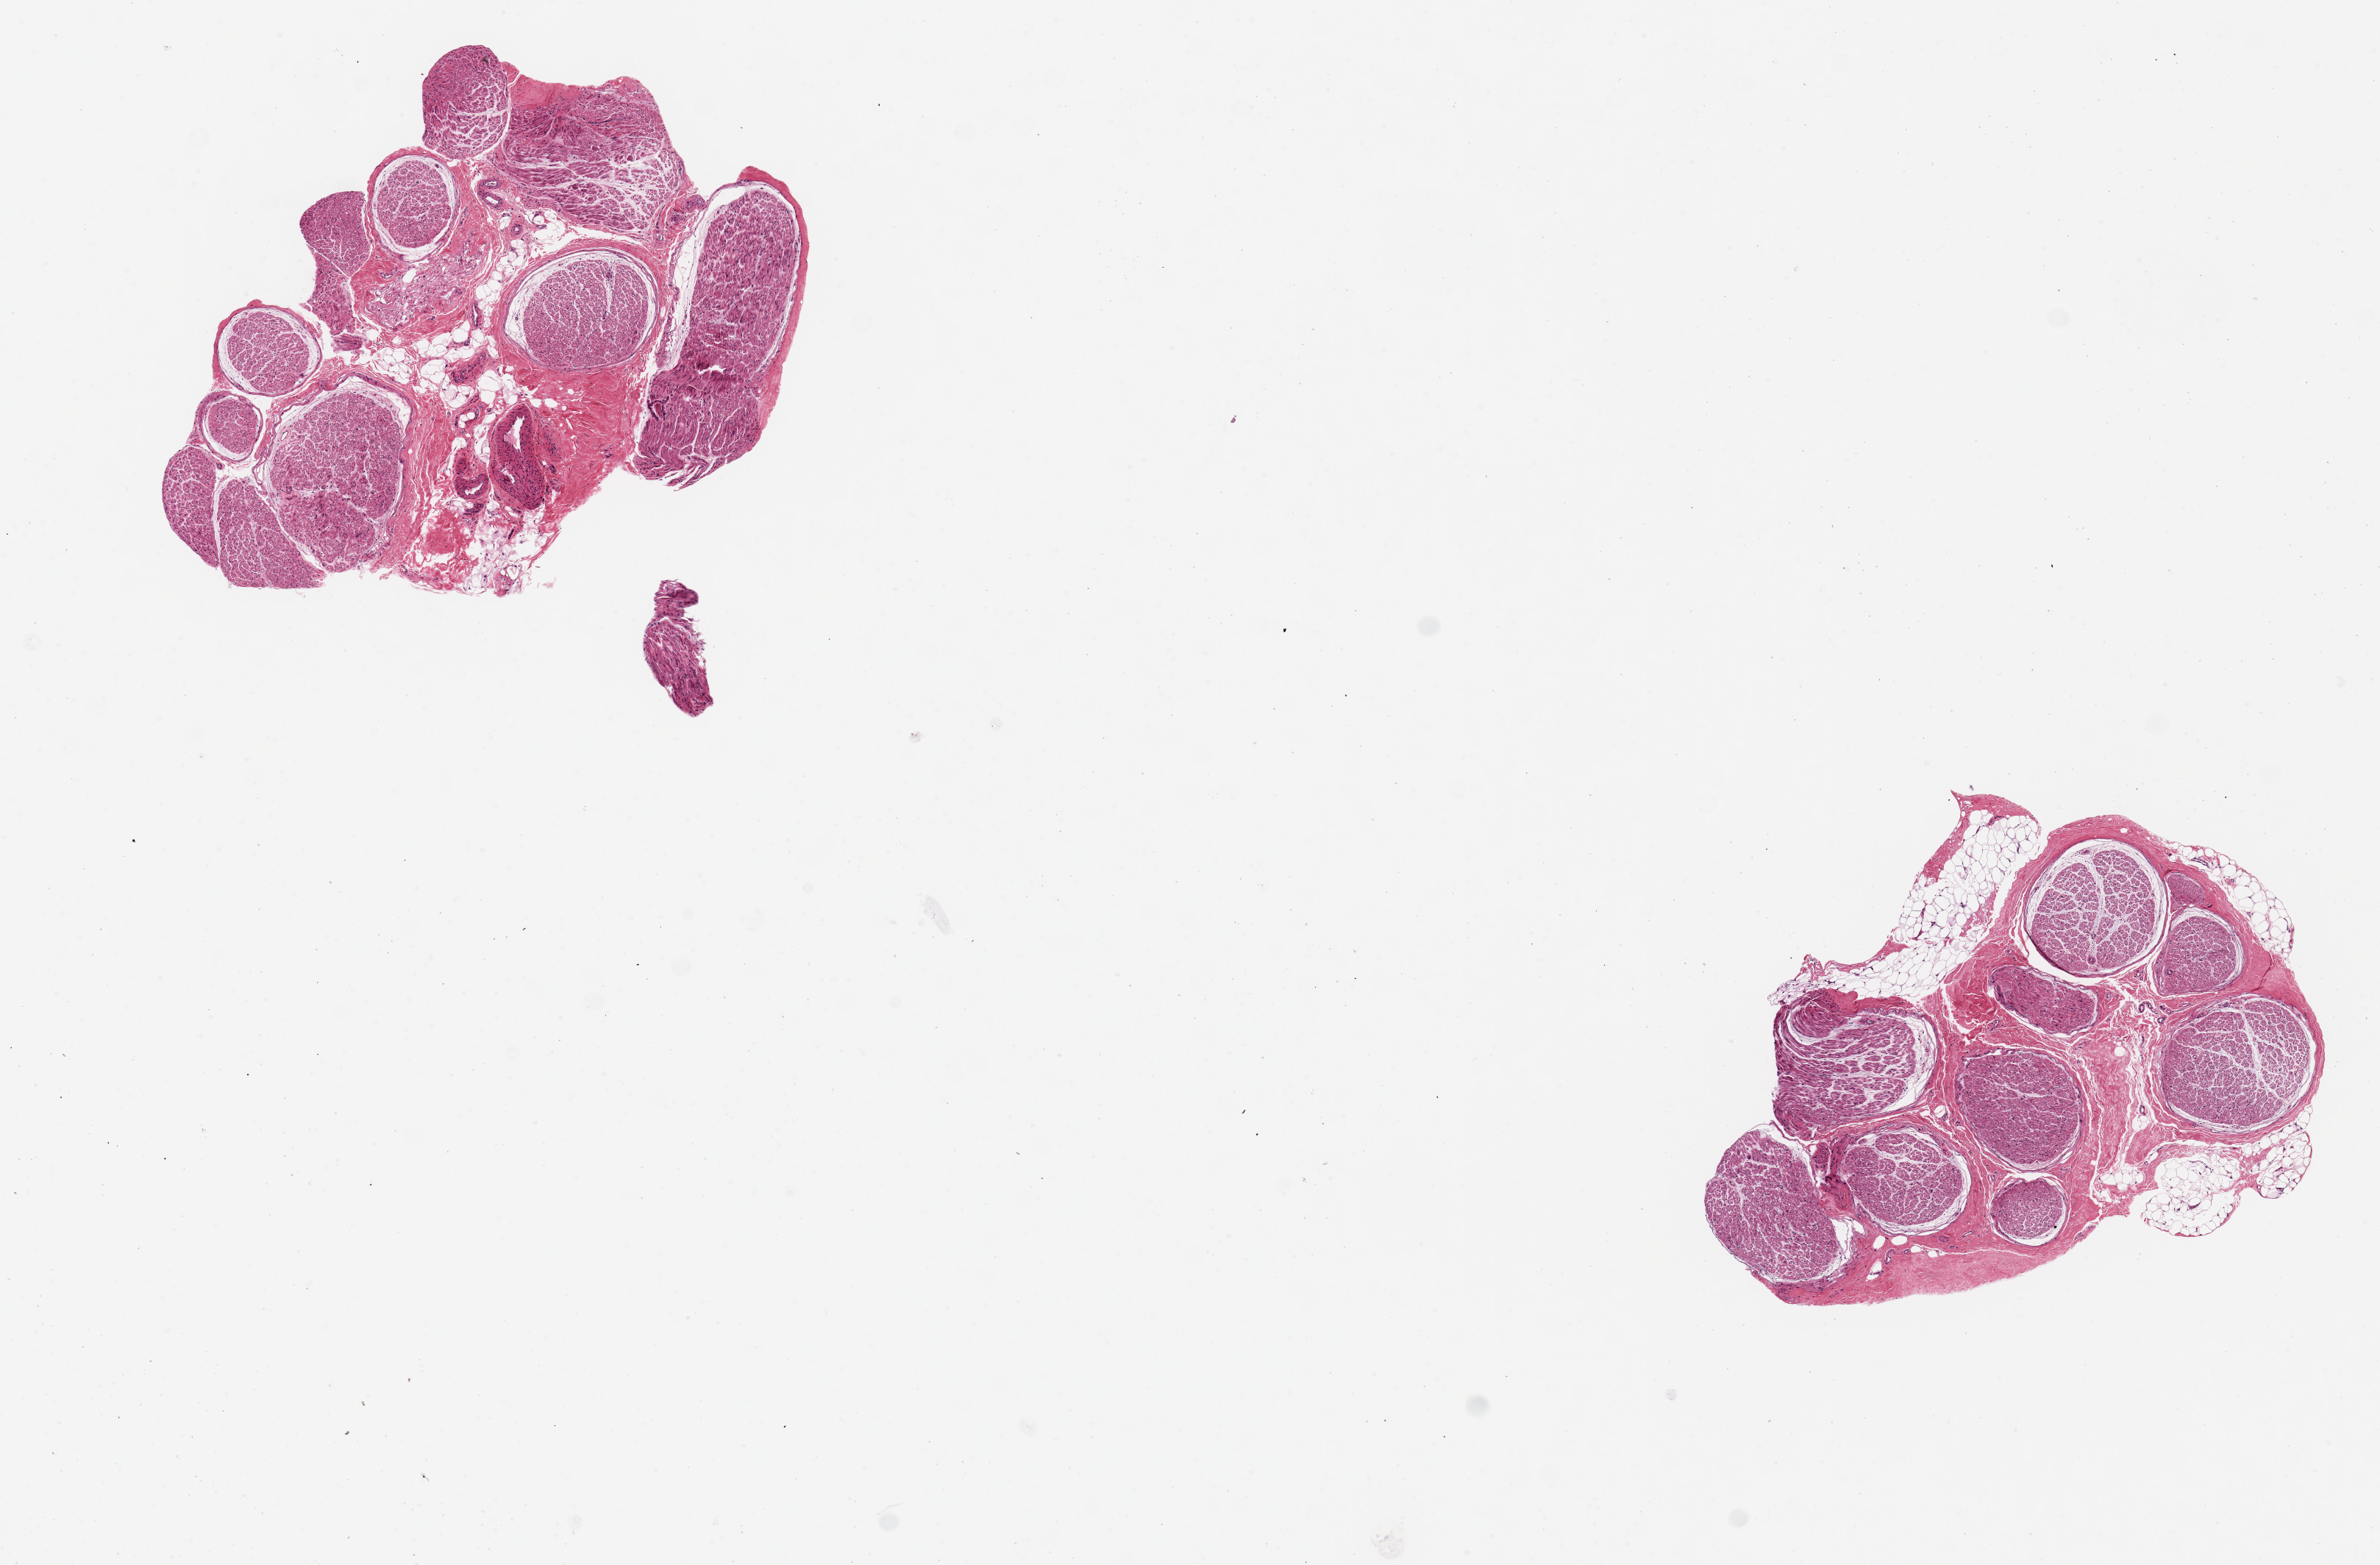
Digitized H&E-stained section, low-resolution overview of the scanned area, about 12.8 x 8.4 mm (acquisition: 20x scan). PAXgene-fixed, paraffin-embedded tissue. Section of tibial nerve (target tissue). Tissue donor sample. Male donor.
Review note (as recorded): 2 pieces ~3.5mm d. Clean. Trace fat adherent on one.